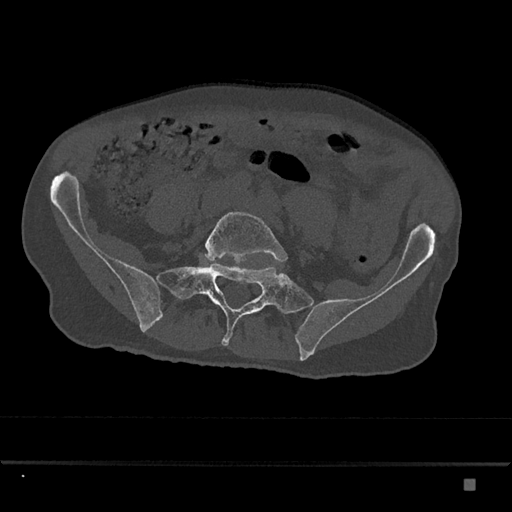
CT including the spine, one axial slice. Bone window (W 1800 / L 400 HU). 0.5 mm slice thickness. 512 × 512 image matrix, field of view 390 × 390 mm. Patient: male, 72 years. Case-level facts recorded for this patient, not image findings: primary cancer: prostate.
Structures marked on this image (semi-automatically segmented with operator editing):
- L5 vertebra: bounding box (x1, y1, x2, y2) in pixels: (205, 211, 287, 266)